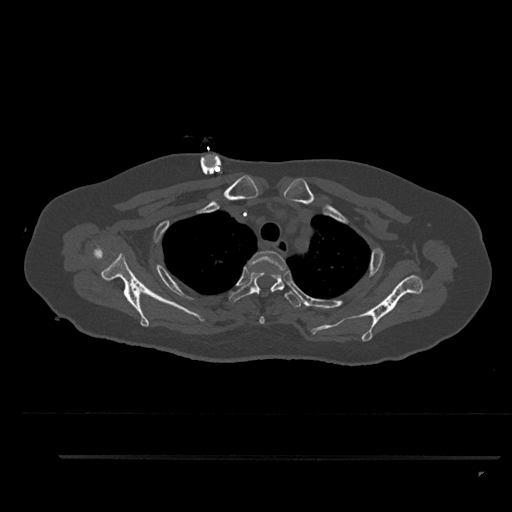
CT including the spine, one axial slice. Position 698 of 797 along the scan axis. Bone window (W 1800 / L 400 HU). 0.5 mm slice thickness. 512 × 512 image matrix, field of view 408 × 408 mm. Female patient, age 44 years. Case-level facts recorded for this patient, not image findings: primary cancer: renal.
Annotated regions visible in this slice (semi-automatic segmentation, software-assisted and operator-edited):
- T2 vertebra: bounding box <248,251,287,324> (left, top, right, bottom; pixels)
- T3 vertebra: <228,271,303,308>